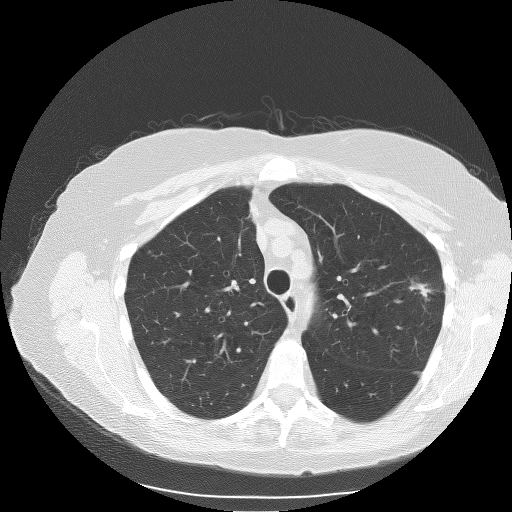
Low-dose screening chest CT, axial slice; baseline screening round; lung window (W 1500 / L -600 HU); lung (sharp) reconstruction kernel (BONE); slice 70 of 106 in the series. Female participant, aged 71 years at enrolment.
Lesion marked by an expert reader, bounding box [x1, y1, x2, y2] px = [404, 278, 440, 312]. Reader record for this screening exam (exam-level; its link to the box is not recorded): non-calcified nodule or mass ≥4 mm, left upper lobe, 15 × 9 mm, spiculated (stellate) margins, soft tissue attenuation. Participant outcome: lung cancer diagnosed 77 days after this screen — adenocarcinoma, NOS, left upper lobe, moderately differentiated (G2), stage IA (AJCC 6th edition), 15 mm at pathology.